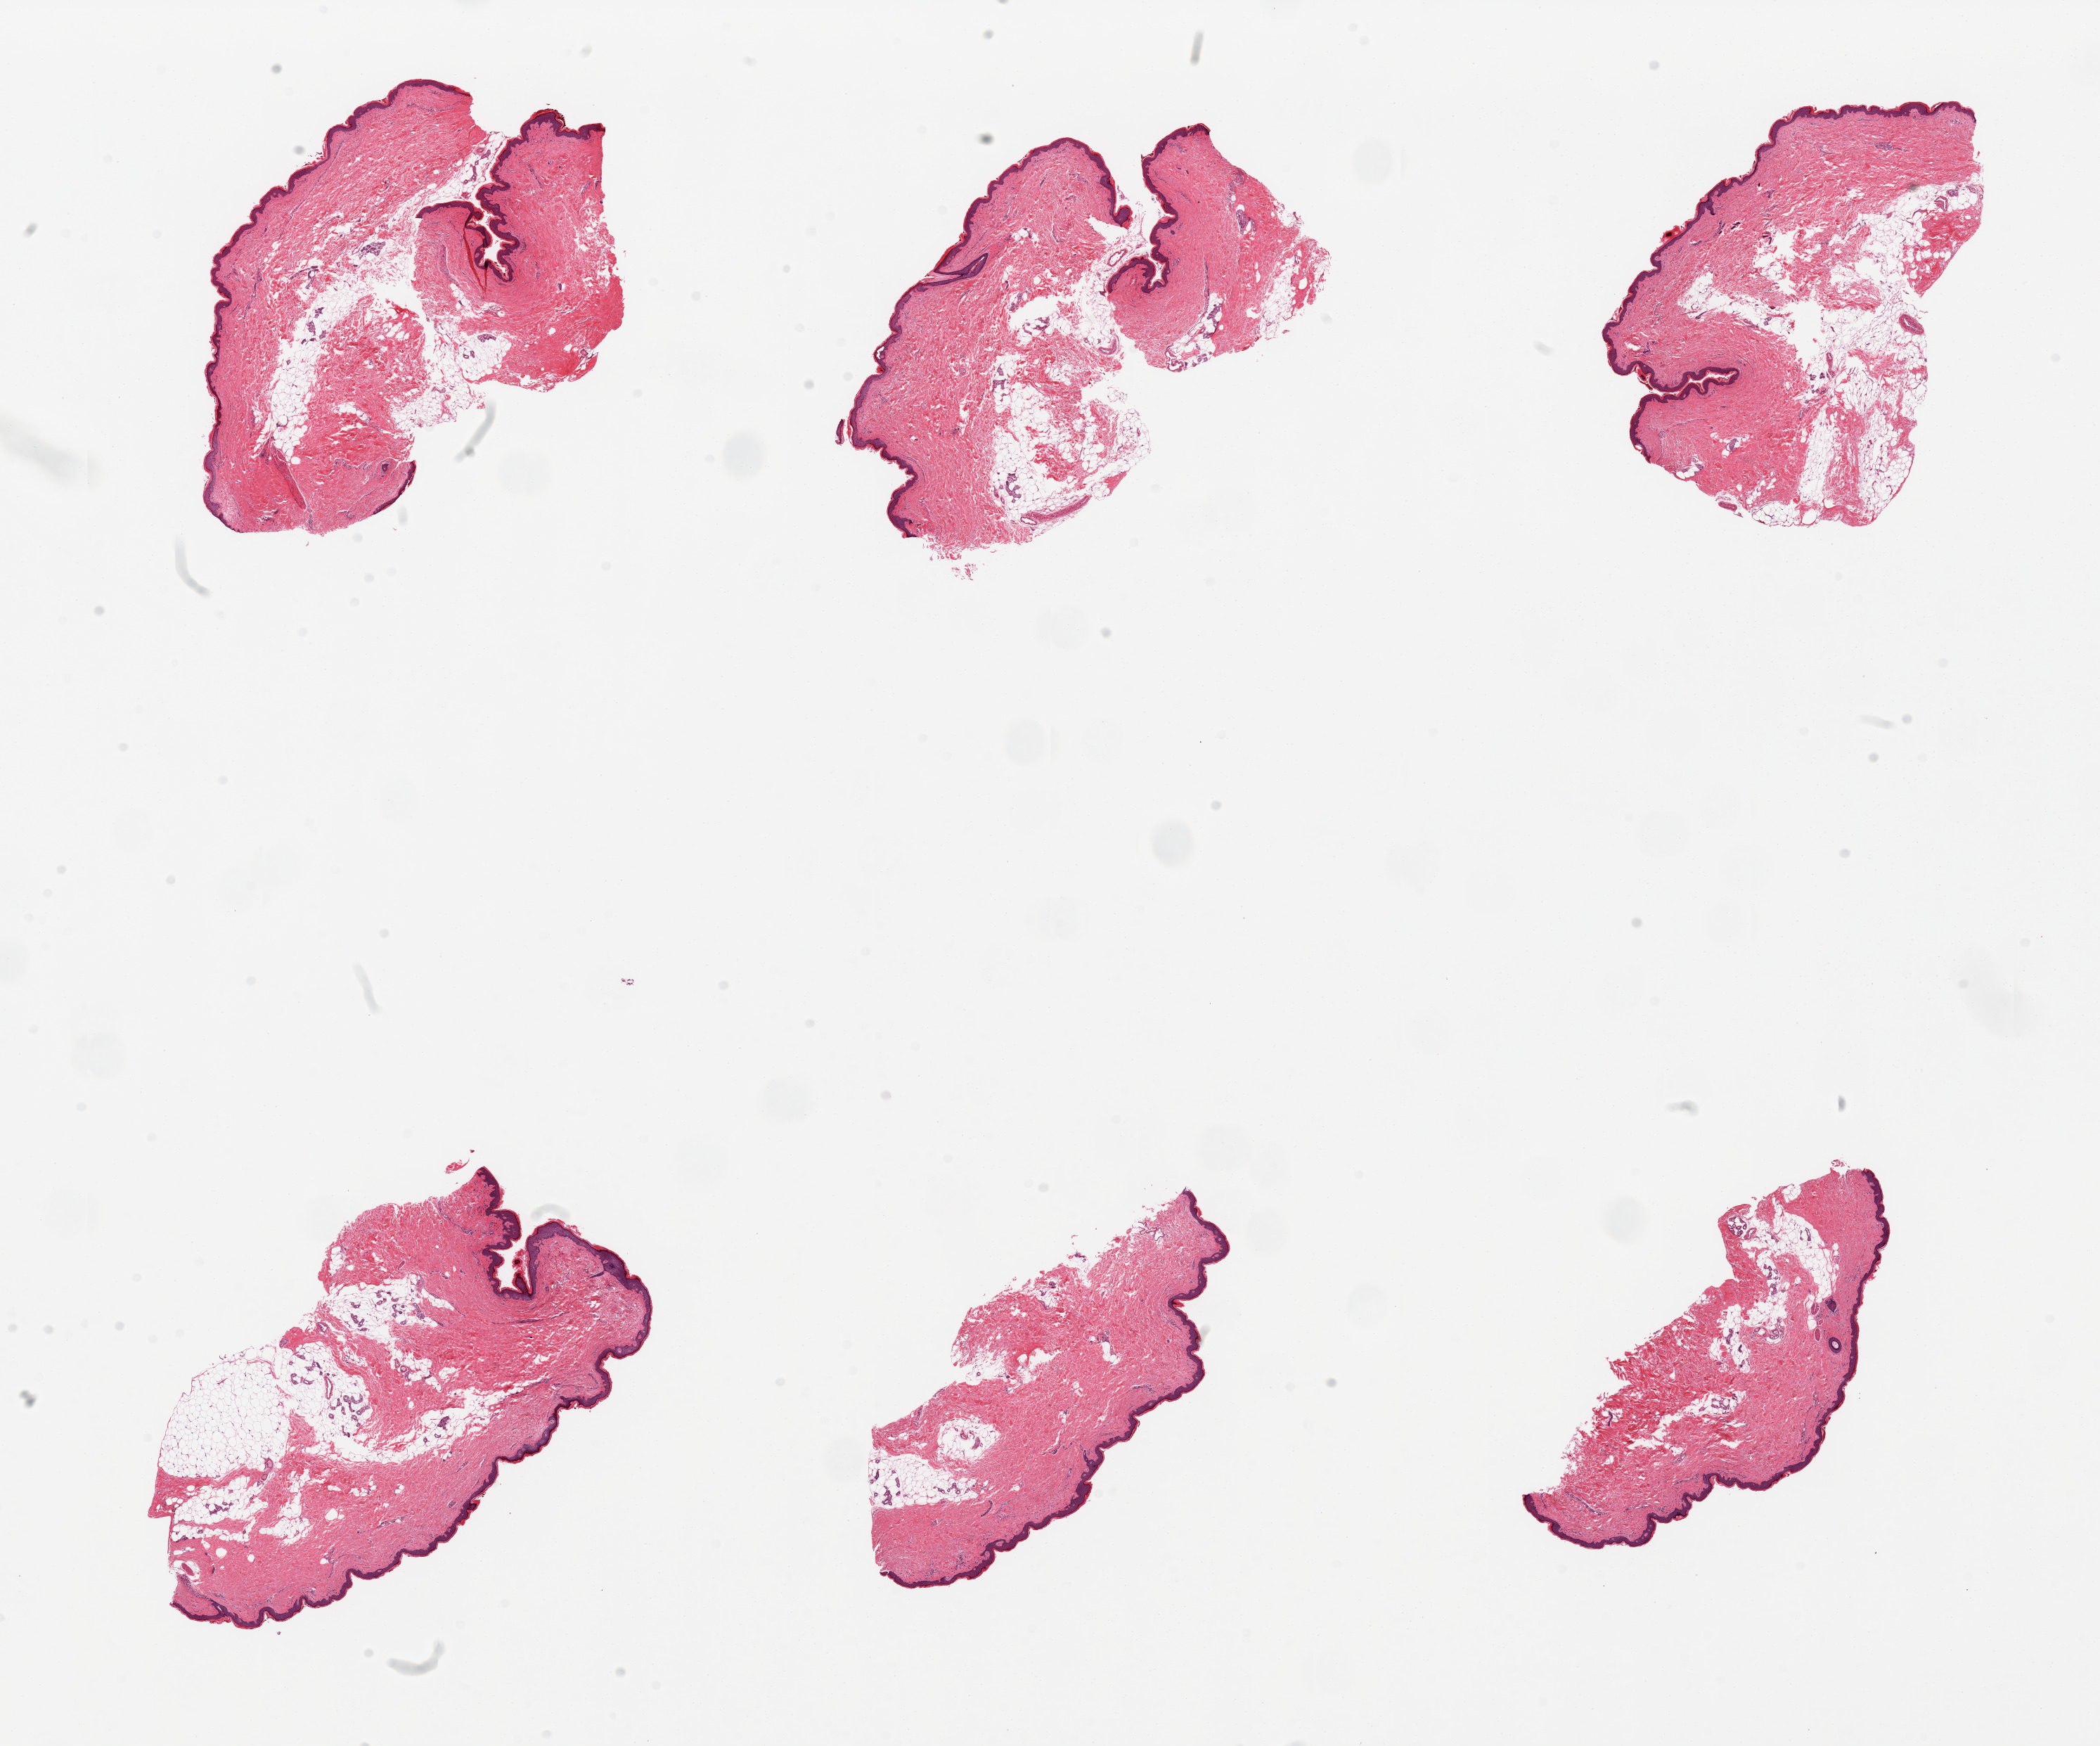
Digitized haematoxylin and eosin-stained section, shown as a low-resolution overview of the whole scanned area (about 23.6 x 19.6 mm), PAXgene-fixed paraffin-embedded (PFPE) section, section of skin of lower leg (target tissue), tissue donor sample. Donor: female.
- reviewer comment on this tissue sample: 6 pieces; up to 30% fat within the dermis